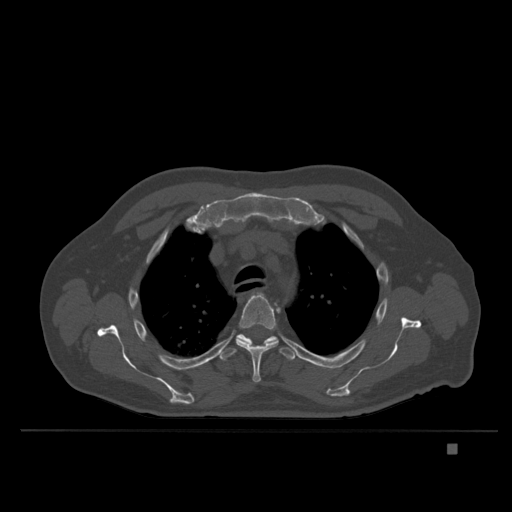
CT including the spine, one axial slice; slice 284 of 435 in the series (ordered by position); bone window (W 1800 / L 400 HU); 512 × 512 image matrix, field of view 434 × 434 mm. Male patient, age 73 years. From the clinical record (not read from this slice): primary cancer: skin.
Outlined on this slice (semi-automatically segmented with operator editing):
- T4 vertebra: bounding box <235,293,280,383> (left, top, right, bottom; pixels)
- T5 vertebra: <220,333,295,361>